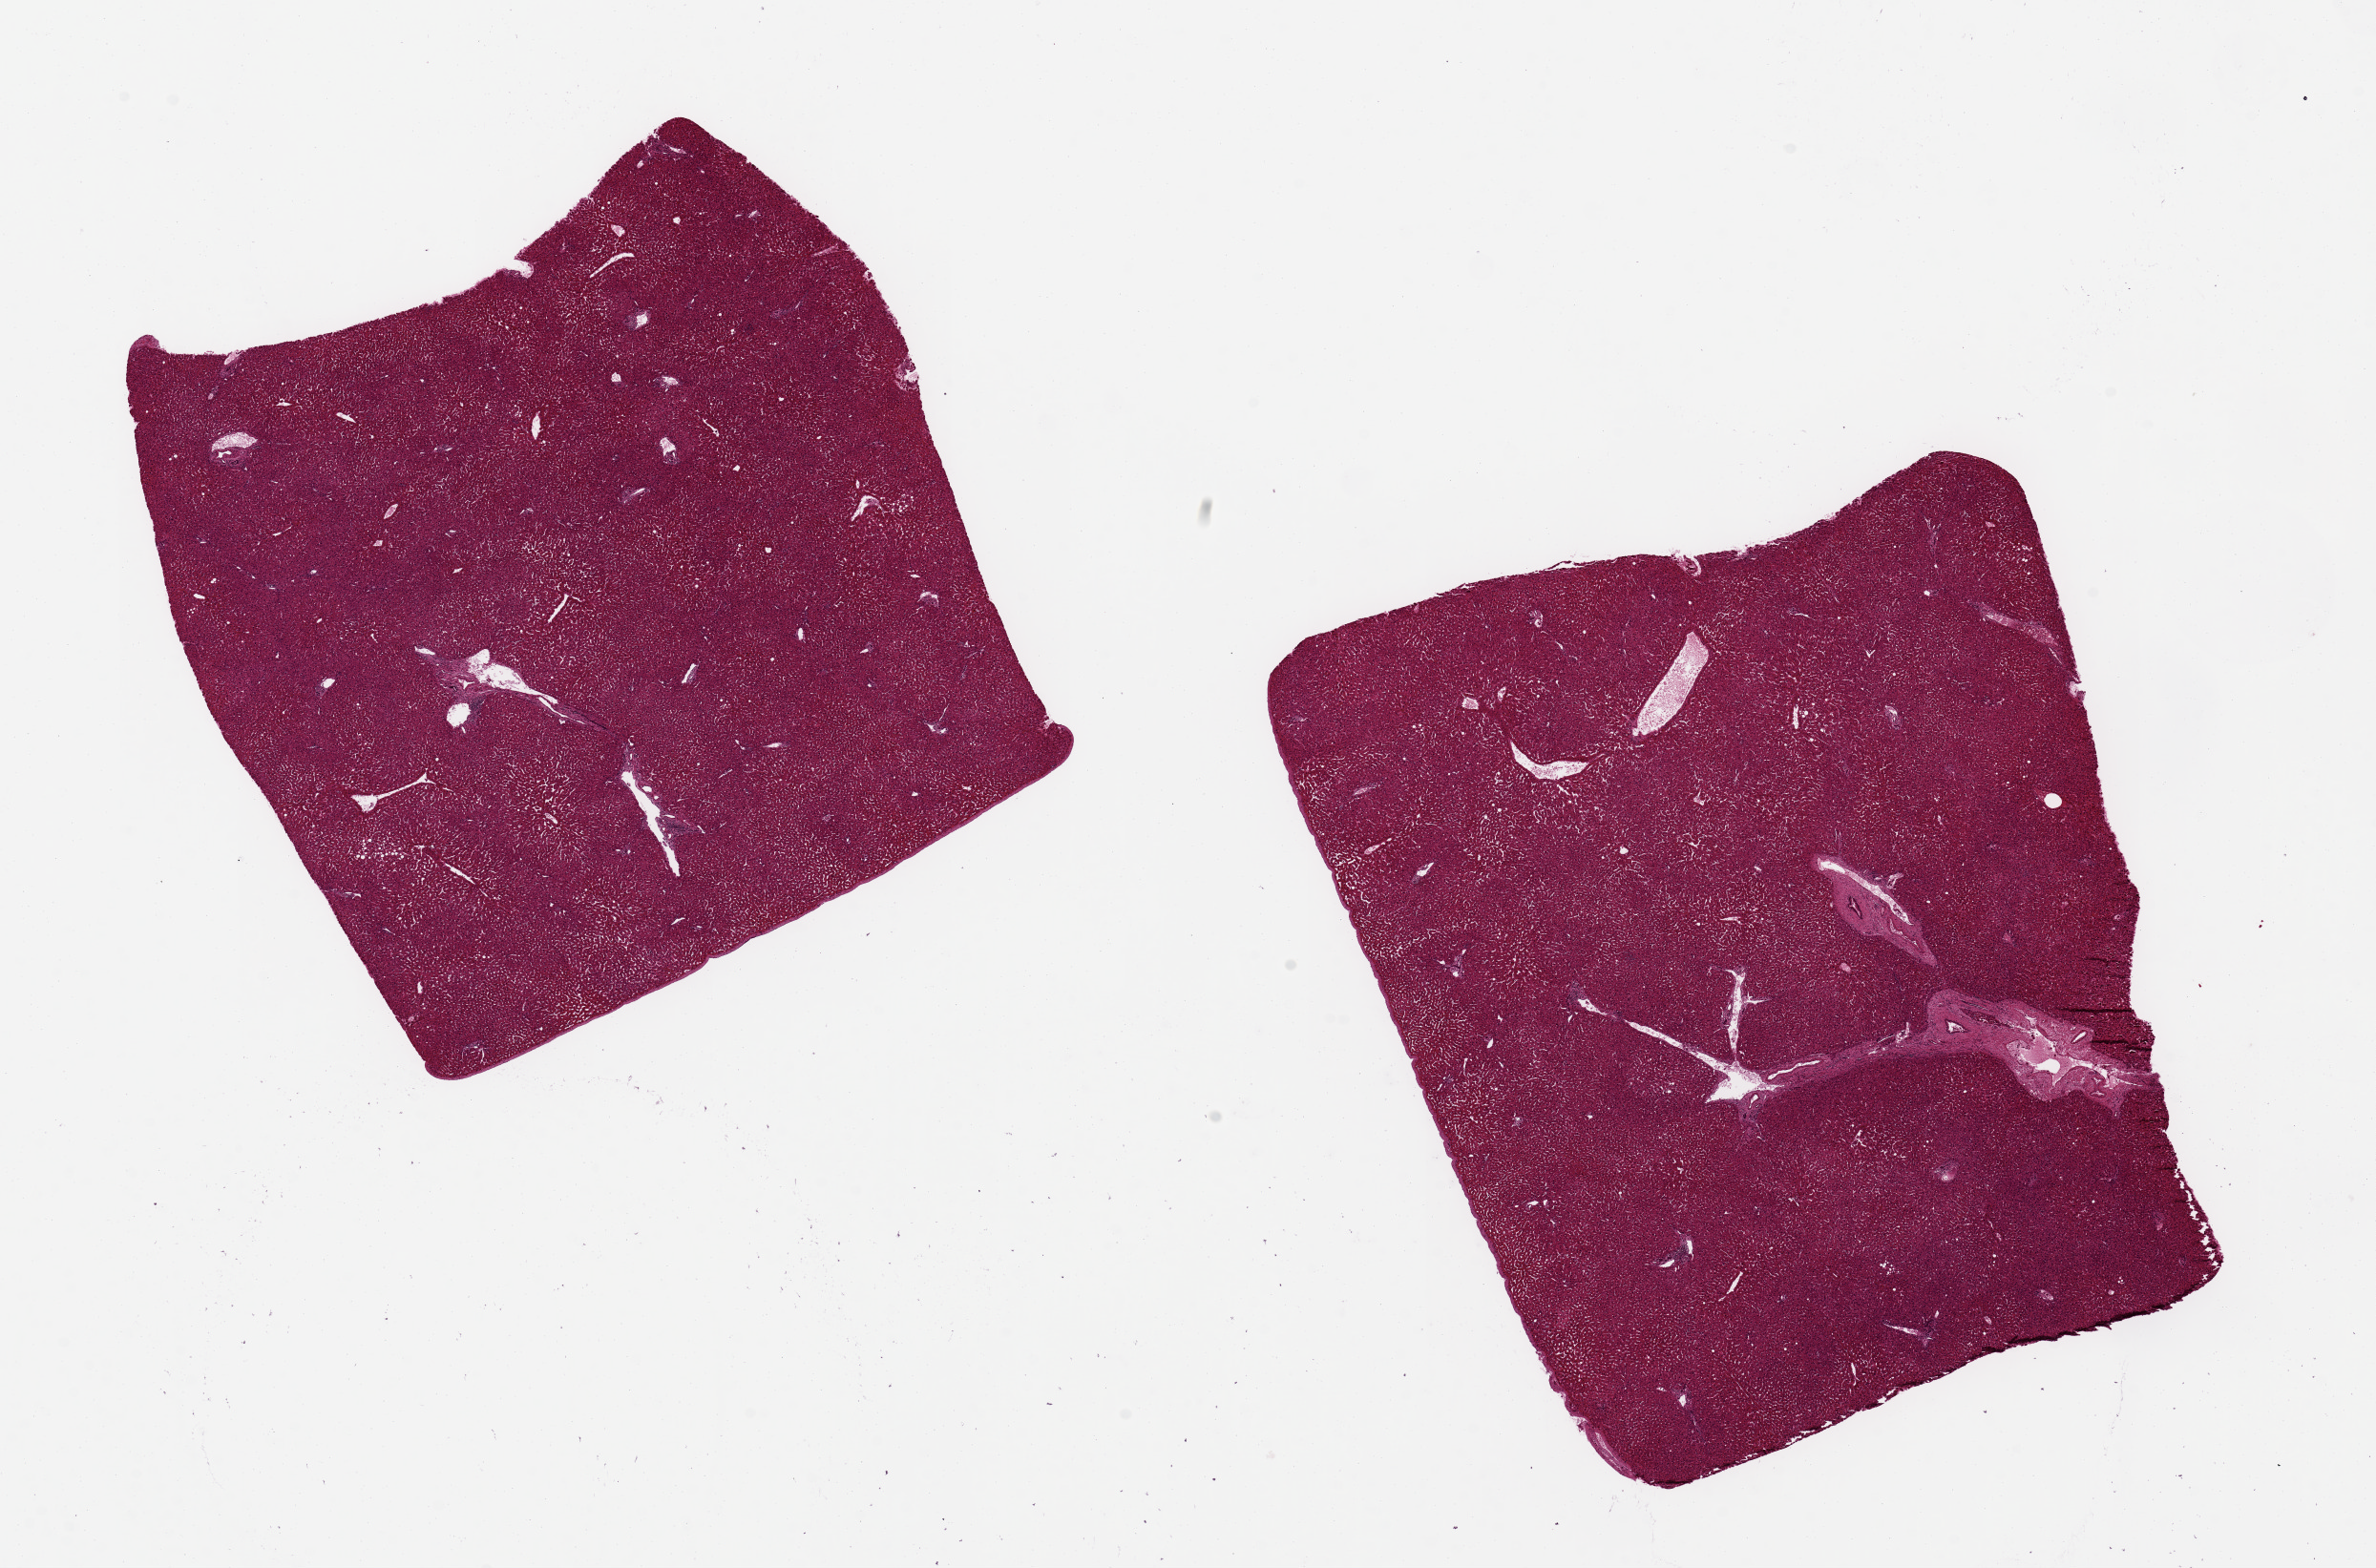
Digitized haematoxylin and eosin-stained section, a low-resolution overview of the entire scanned area, about 19.7 x 13.0 mm (acquisition: 20x scan). PAXgene-fixed paraffin-embedded (PFPE) section. Section of liver (target tissue). Tissue donor sample. Donor: male.
• pathologist's review note for this sample: 2 pieces ~8x7mm. Minimal steatosis